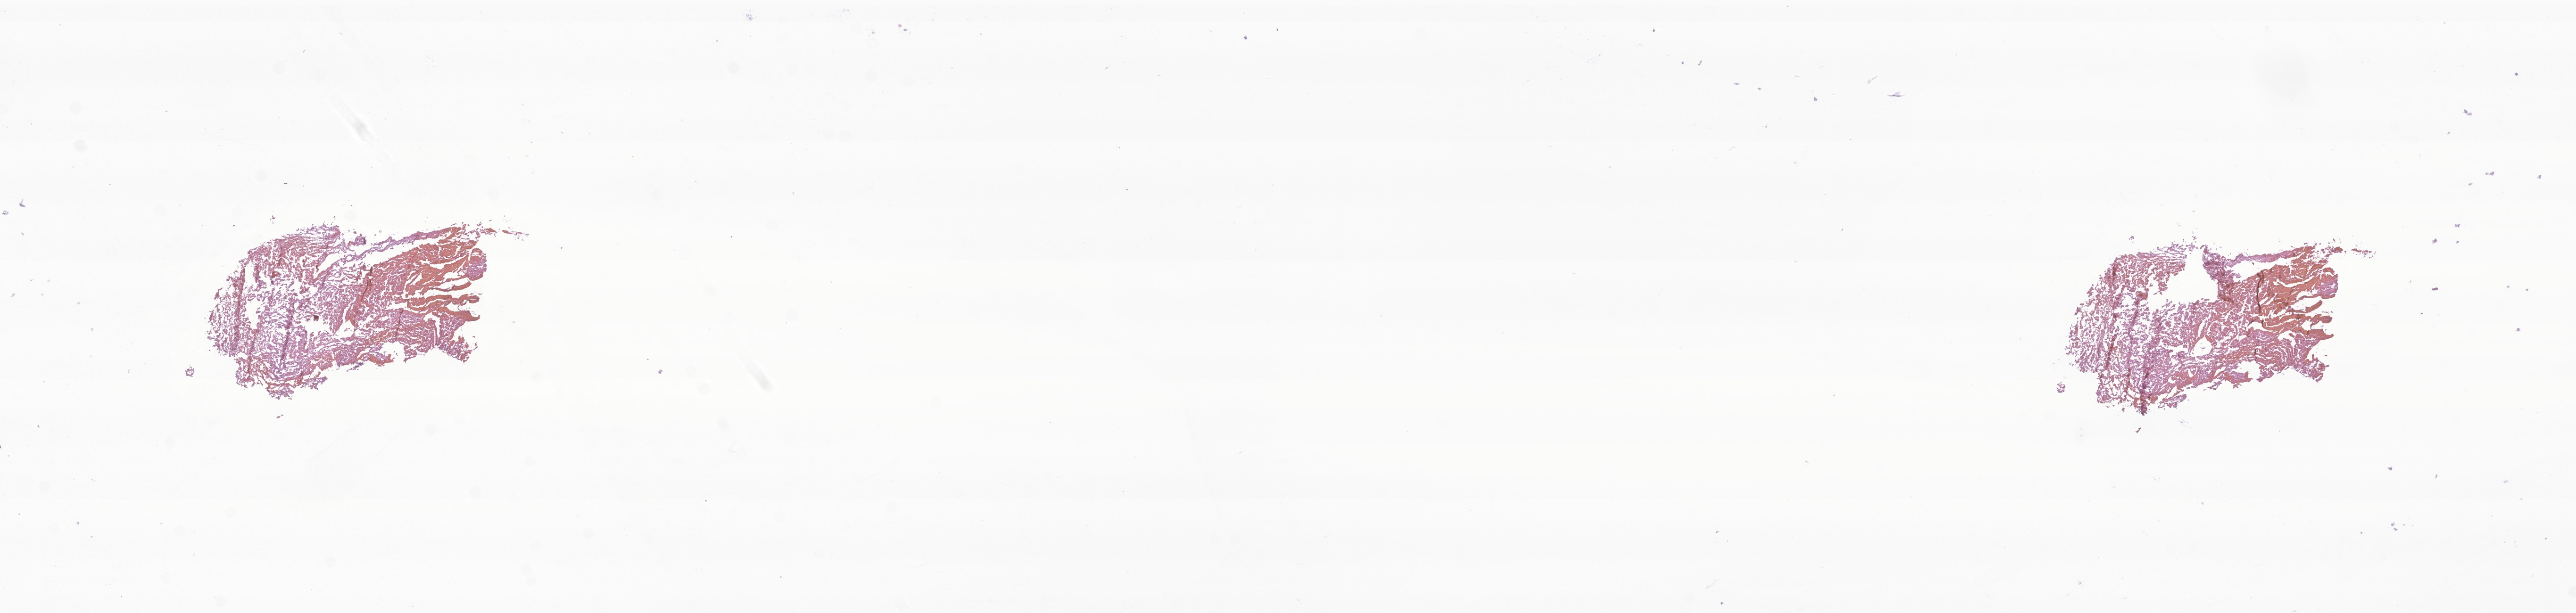
Whole-slide image, haematoxylin and eosin stain of tumor tissue from the cerebral ventricle, shown as a low-resolution overview of the whole scanned area (about 23.0 x 5.5 mm). Cryosection (OCT / tissue freezing medium). Male patient, age 213 months (17 years 9 months).
* diagnosis (ICD-O-3 morphology term): Astrocytoma, NOS